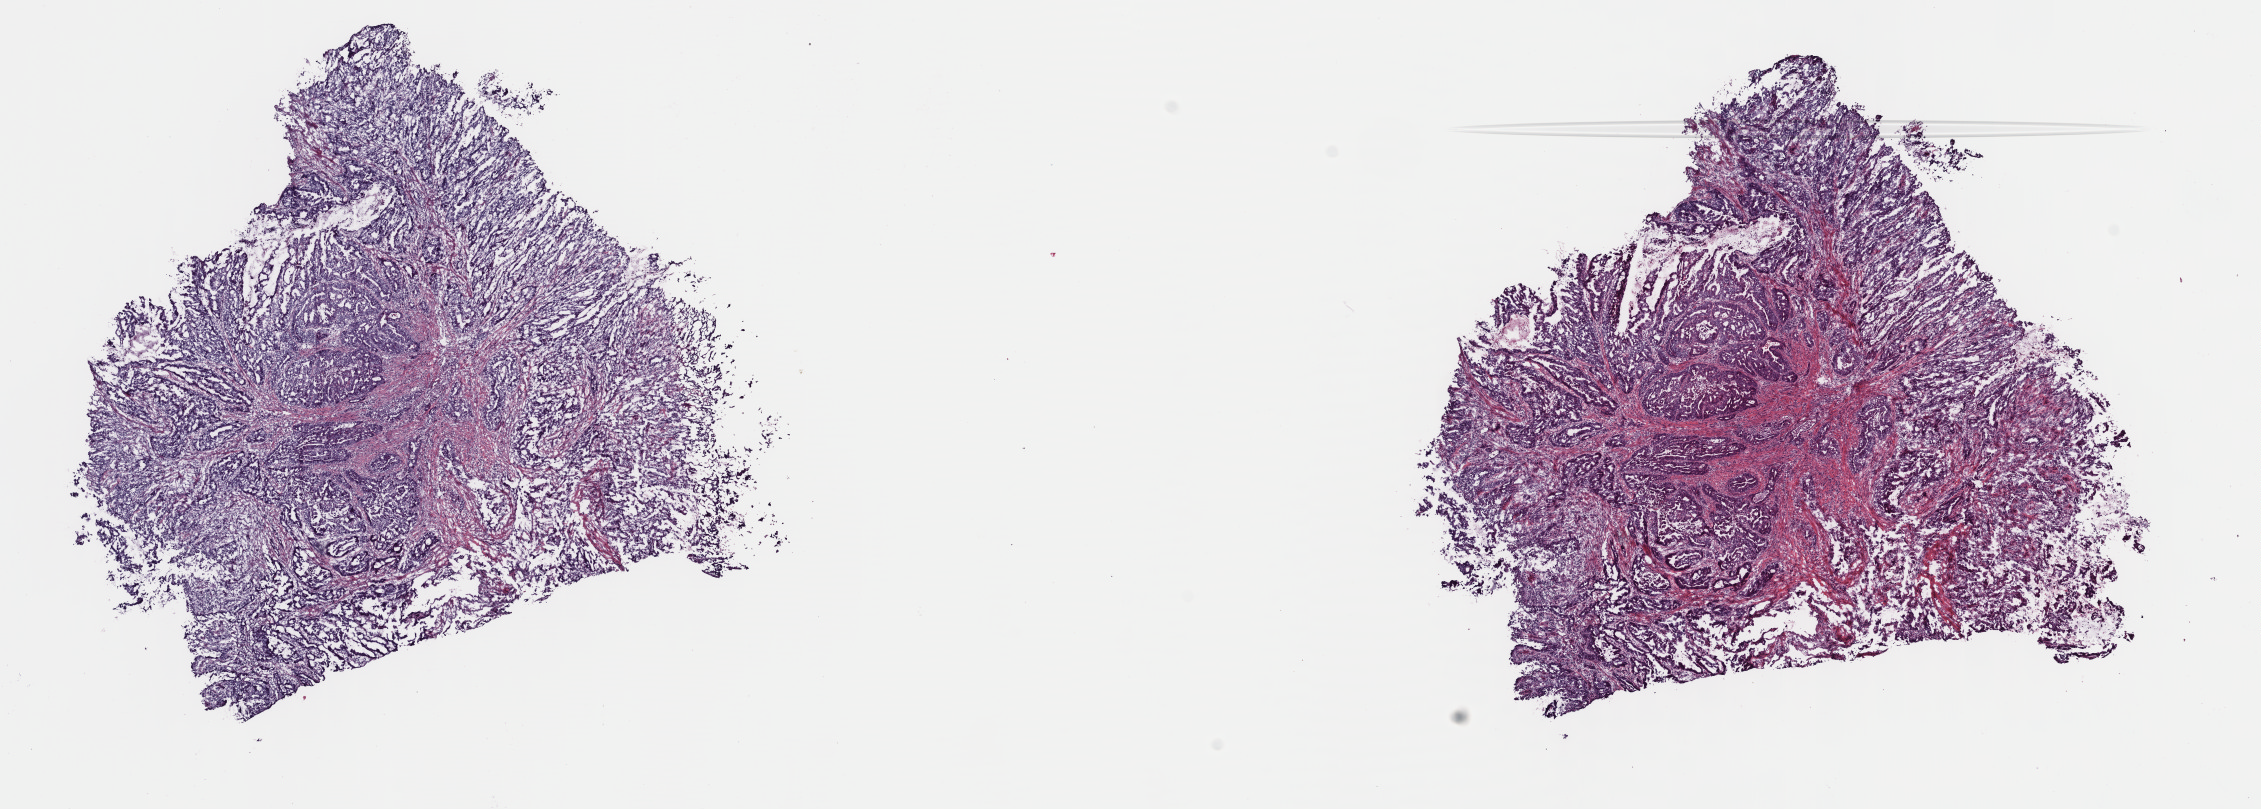
Hematoxylin and eosin (H&E) stained whole-slide image, whole scanned area (about 17.8 x 6.4 mm, from a 40x scan) shown as a low-resolution overview, frozen section from the top of the tissue portion, primary tumour sample from the esophagus. Patient: female, age at initial diagnosis 56 years. Histologic grade: GX (grade cannot be assessed). Composition of this section per pathologist review: tumour cells 98%, tumour nuclei 65%, normal cells 0%, stromal cells 0%, necrosis 2%. Inflammatory infiltration, as recorded: lymphocyte infiltration 0%, monocyte infiltration 0%, neutrophil infiltration 0%.
TNM: T2 N1 M0. Diagnosis: Adenocarcinoma, NOS (lower third of esophagus). Lymph nodes positive (case pathology): 2 of 11 examined. AJCC pathologic stage: IIB.